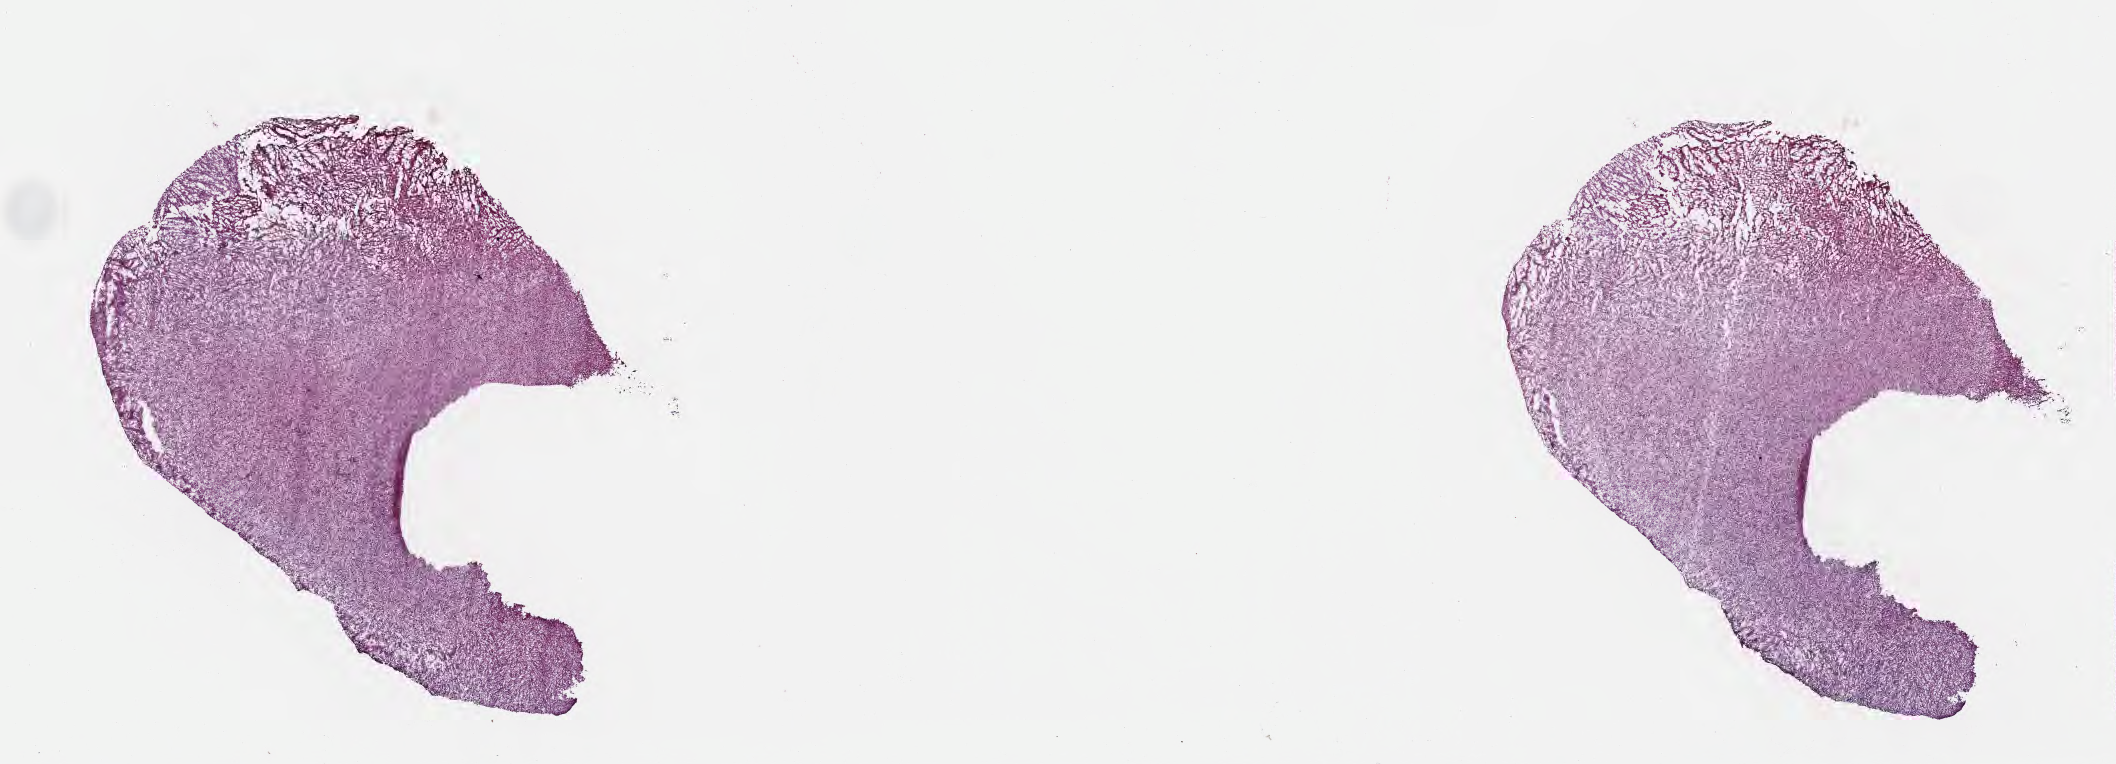
Digitized H&E-stained section — low-resolution overview of the scanned area, about 17.1 x 6.2 mm; frozen section; specimen: primary tumor; site: brain. Male, age 59 years at initial diagnosis. Slide review estimates, as recorded: tumor cells 93%, tumor nuclei 96%, stromal cells 3%, necrosis 0%, normal cells 4%. Infiltration values recorded for this section: lymphocyte infiltration 0%, monocyte infiltration 0%, neutrophil infiltration 0%.
Diagnosis: Glioblastoma, NOS.